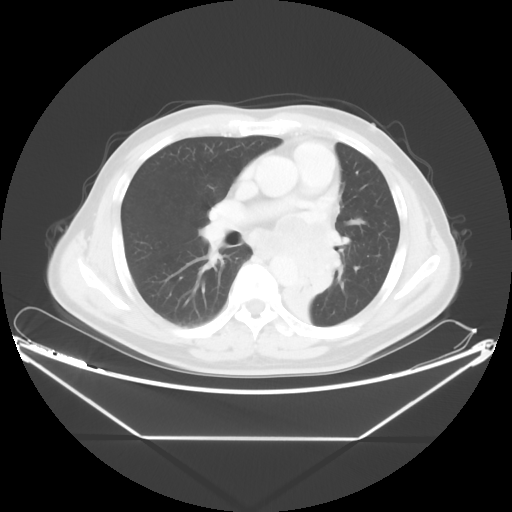
Chest CT, one axial slice. Slice 25 of 48 in the series (ordered by position). Reconstruction kernel STANDARD. Lung window (W 1500 / L -600 HU). 5 mm slice thickness. 512 × 512 image matrix, field of view 438 × 438 mm. Male patient, age 58 years. From the clinical record (not read from this slice): clinical TNM (as recorded): T3 N3 M0.
Annotated regions visible in this slice (bounding box drawn by a radiologist):
- lung tumour (recorded histology: squamous cell carcinoma): bounding box (x1, y1, x2, y2) in pixels: (279, 236, 355, 345)